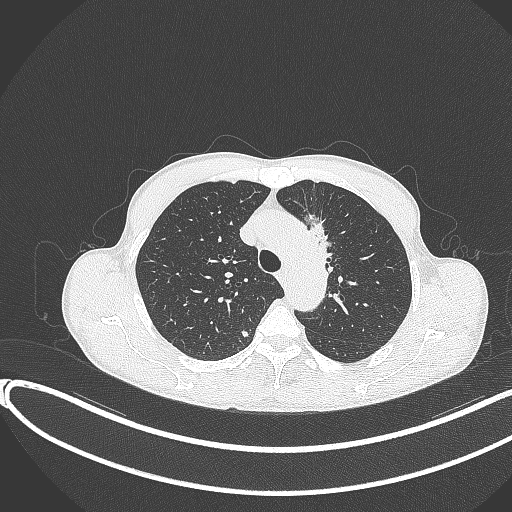
Chest CT, one axial slice. Position 283 of 374 along the scan axis. Reconstruction kernel B70f. 120 kVp. Lung window (W 1500 / L -600 HU). 1 mm slice thickness. 512 × 512 image matrix, field of view 400 × 400 mm. Male patient, age 58 years. From the clinical record (not read from this slice): clinical TNM (as recorded): T1c N1 M0.
Outlined on this slice (bounding box drawn by a radiologist):
- lung tumour (recorded histology: adenocarcinoma): bounding box [x1, y1, x2, y2] px = [298, 214, 331, 275]